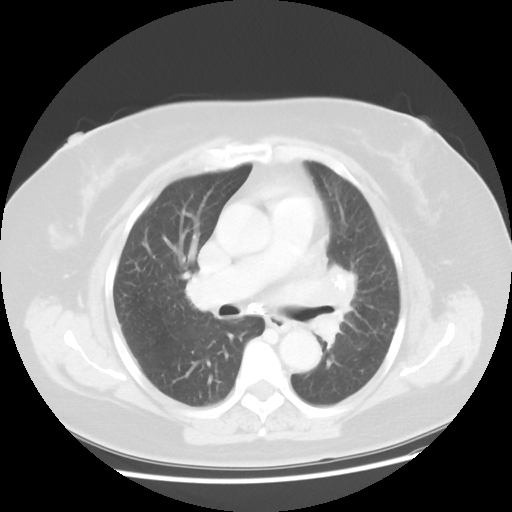
Chest CT, one axial slice. Position 26 of 49 along the scan axis. 120 kVp. Lung window (W 1500 / L -600 HU). 512 × 512 image matrix. Female patient, age 58 years. From the clinical record (not read from this slice): clinical TNM (as recorded): T4 N3 M0; histopathological grade: G3.
Outlined on this slice (bounding box drawn by a radiologist):
- lung tumour (recorded histology: small cell carcinoma): bounding box [x1, y1, x2, y2] px = [295, 259, 370, 350]